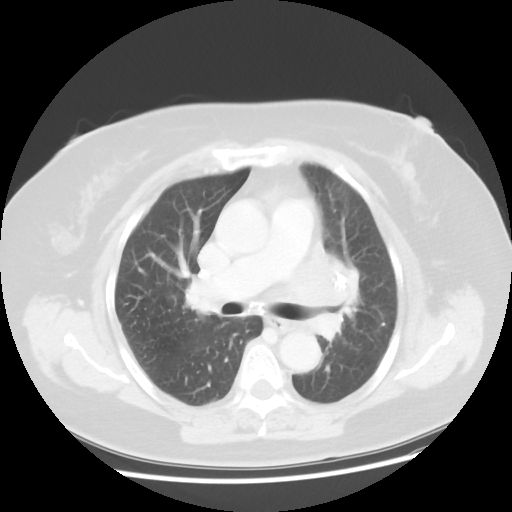
Chest CT, one axial slice; position 27 of 49 along the scan axis; reconstruction kernel STANDARD; lung window (W 1500 / L -600 HU); 5 mm slice thickness; 512 × 512 image matrix, field of view 374 × 374 mm. Patient: female, 58 years. Case-level facts recorded for this patient, not image findings: clinical TNM (as recorded): T4 N3 M0.
Outlined on this slice (bounding box drawn by a radiologist):
- lung tumour (recorded histology: small cell carcinoma): bounding box [x1, y1, x2, y2] px = [286, 249, 375, 362]